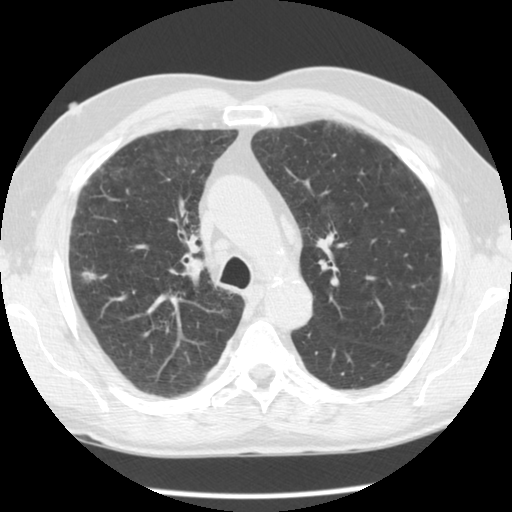
Low-dose screening chest CT, one axial slice; position 78 of 113 along the scan axis; reconstruction kernel STANDARD; lung window (W 1500 / L -600 HU); 512 × 512 image matrix.
Annotated regions visible in this slice (expert manual segmentation):
- lesion 2 (nodule): bounding box <81,271,97,281> (left, top, right, bottom; pixels)